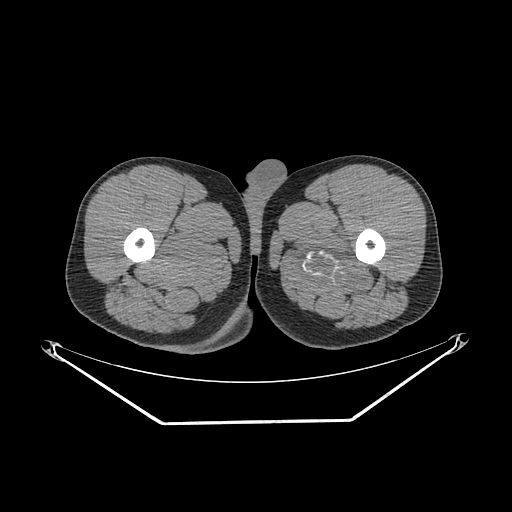
CT of an extremity soft-tissue mass (from a PET/CT study), one axial slice. Slice 254 of 267 in the series (ordered by position). Soft-tissue window (W 400 / L 40 HU). 3.75 mm slice thickness. 512 × 512 image matrix, field of view 500 × 500 mm. Male patient. From the clinical record (not read from this slice): histological type: extraskeletal osteosarcoma; grade: high; site of the primary tumour: left adductur.
Annotated regions visible in this slice (expert contour drawn on MRI and transferred to this co-registered scan by the dataset authors):
- gross tumour volume (mass): bounding box (x1, y1, x2, y2) in pixels: (288, 221, 378, 296)